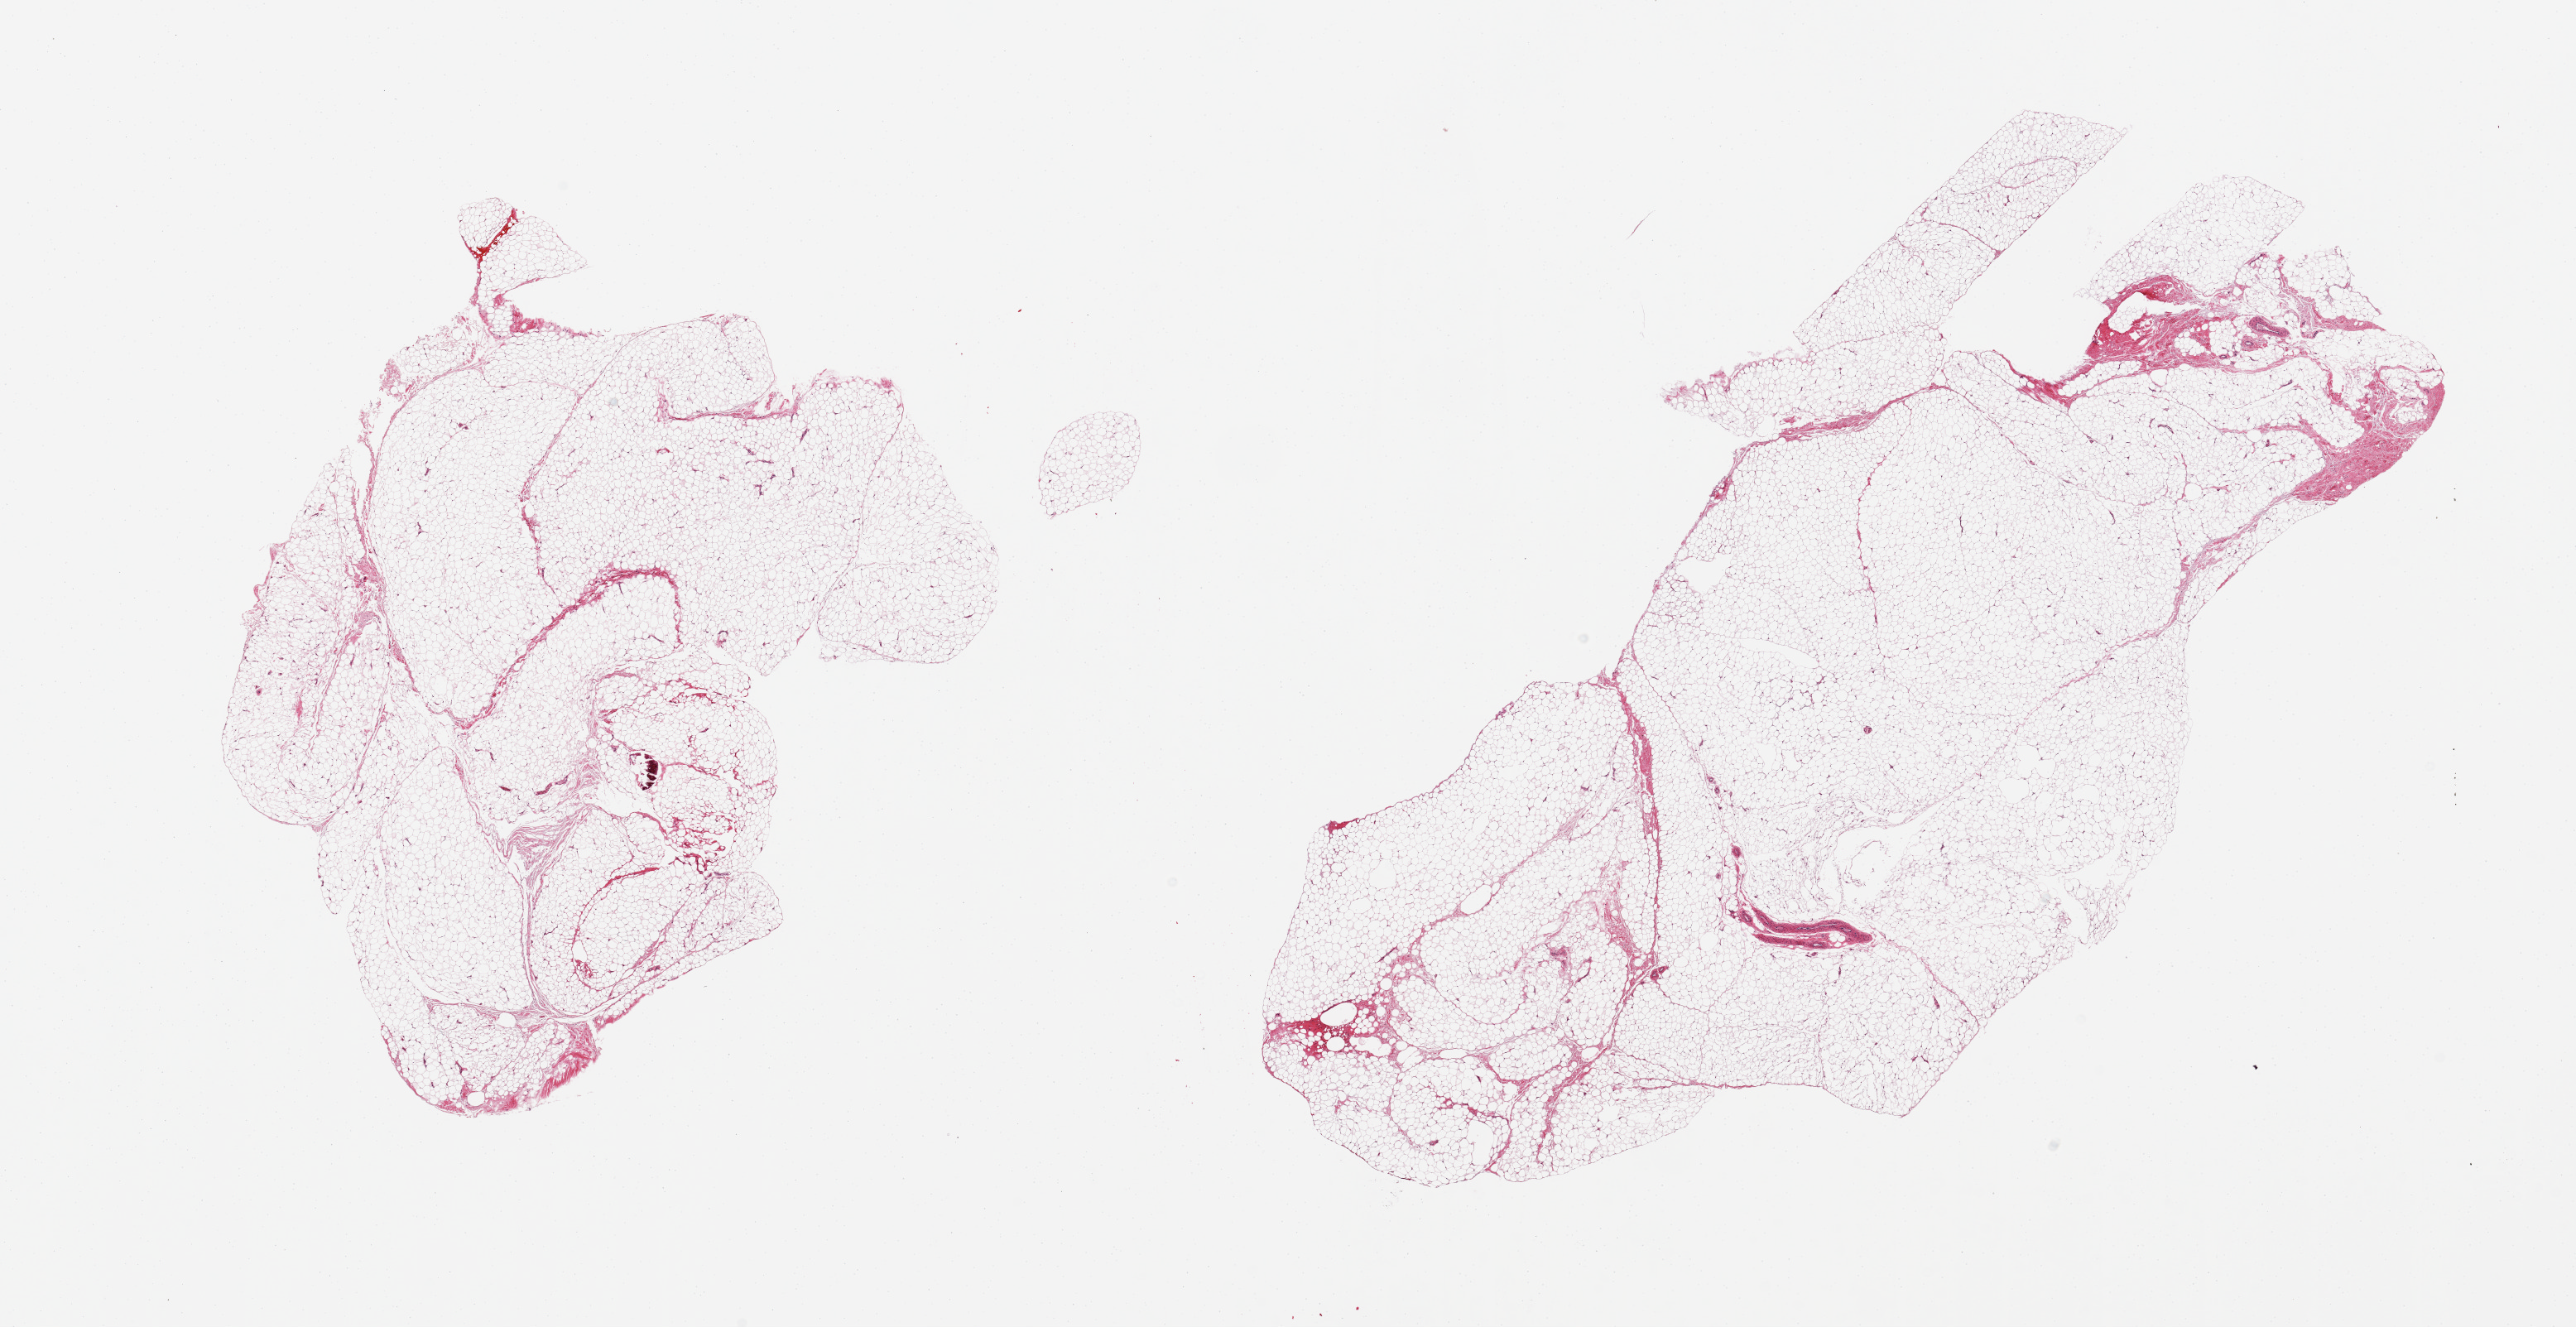
Whole-slide image, haematoxylin and eosin stain — a low-resolution overview of the entire scanned area, about 24.6 x 12.7 mm, PAXgene-fixed, paraffin-embedded tissue, target tissue: adipose tissue, donor tissue sample. Donor sex: male.
• pathologist's review note for this sample: 2 pieces